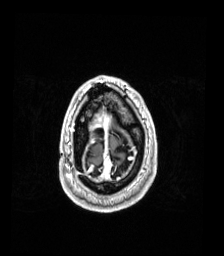
Brain MRI from a brain-tumour surgery series, one axial slice. Slice 25 of 192 in the series (ordered by position). T1-weighted post-contrast. 1 mm slice thickness. 224 × 256 image matrix, field of view 224 × 256 mm. Case-level facts recorded for this patient, not image findings: histopathology: Astrocytoma; WHO grade: 4; IDH mutation: yes; tumour location: Right Frontal.
Outlined on this slice (manually delineated by an expert):
- previous resection cavity: bounding box [x1, y1, x2, y2] px = [96, 129, 103, 135]